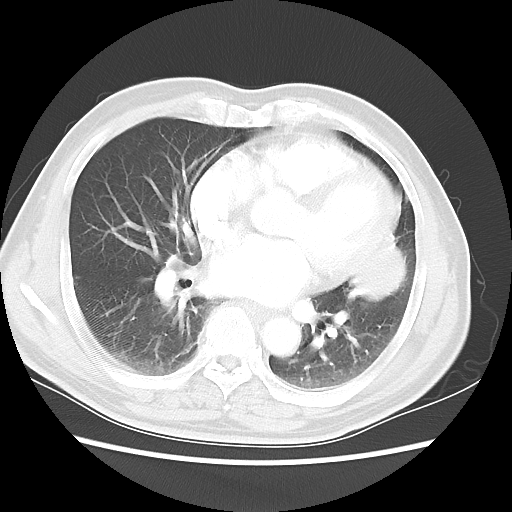
Chest CT, one axial slice. Reconstruction kernel LUNG. 120 kVp. Lung window (W 1500 / L -600 HU). 5 mm slice thickness. 512 × 512 image matrix. Male patient, age 69 years. Case-level facts recorded for this patient, not image findings: clinical TNM (as recorded): T3 N1 M1a.
Annotated regions visible in this slice (rectangle marked by the reading radiologist):
- lung tumour (recorded histology: squamous cell carcinoma): bounding box [x1, y1, x2, y2] px = [349, 230, 419, 319]